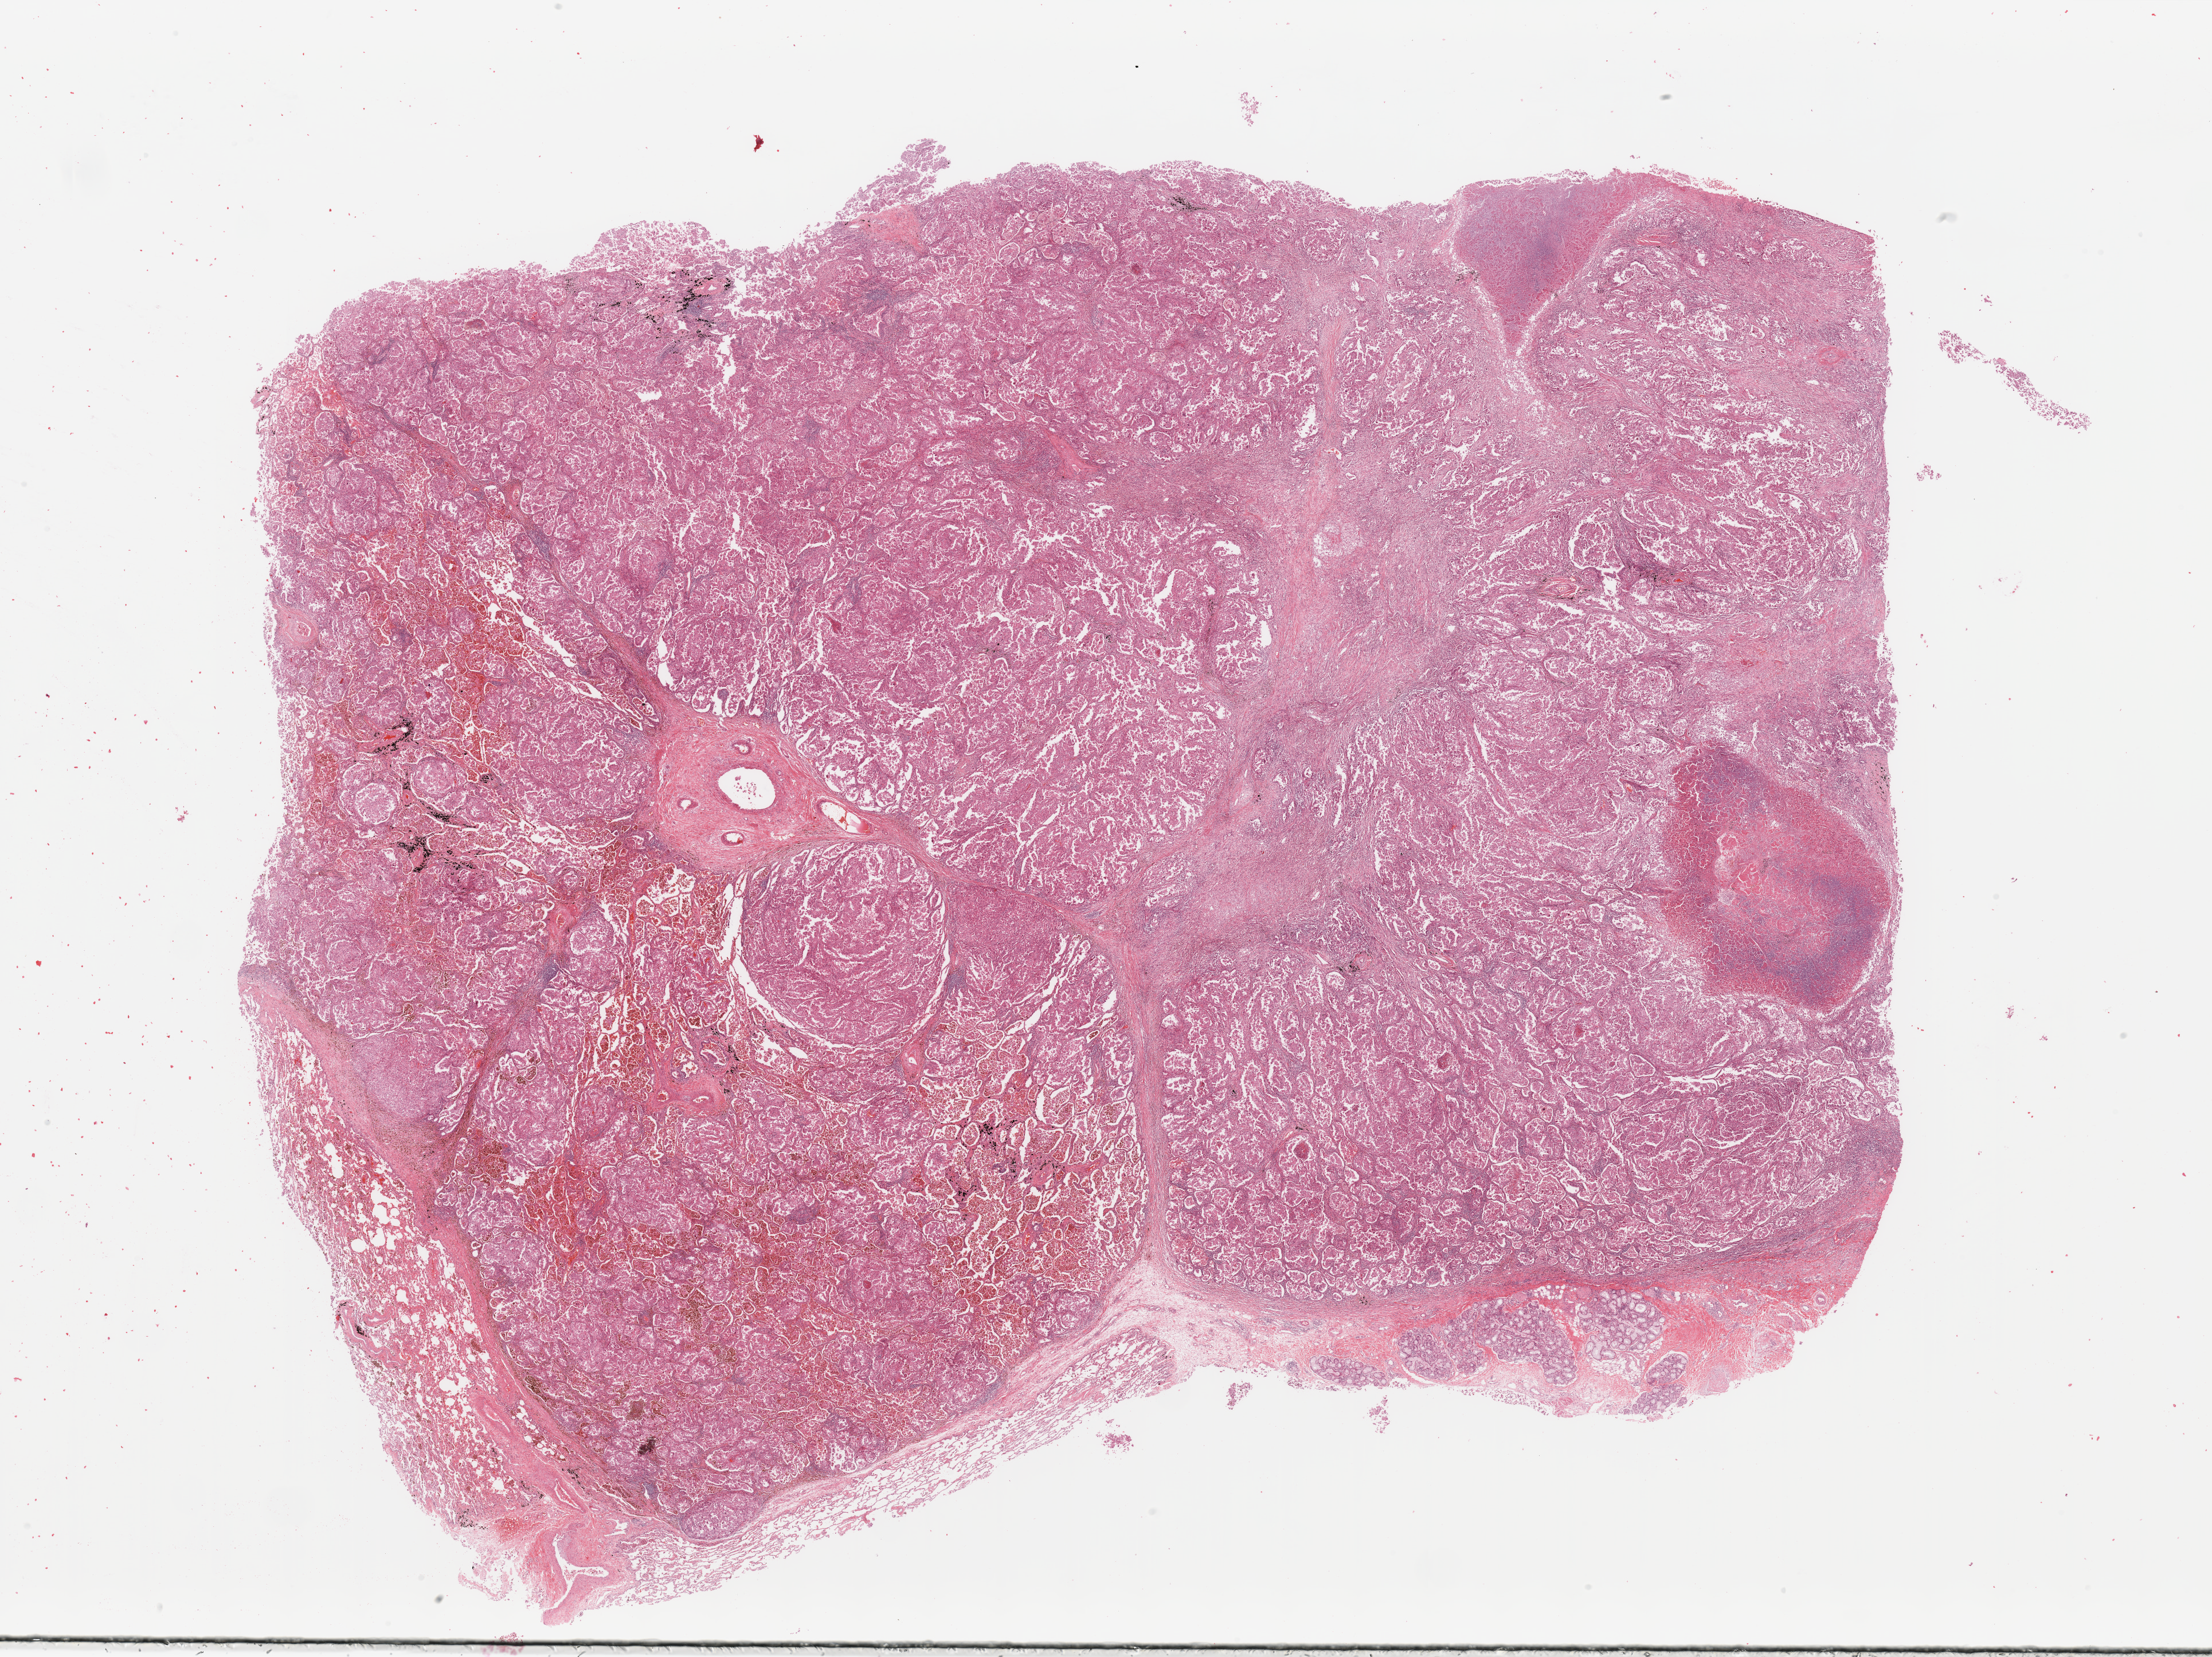
Digitized H&E tissue section (whole slide) — a low-resolution overview of the entire scanned area, about 30.5 x 22.9 mm (slide scanned at 20x); tumour tissue sample, lung. Patient: male, age 55 years. Histologic grade: G2 (moderately differentiated).
Histologic diagnosis: Adenocarcinoma, NOS. AJCC pathologic stage: IIIA.